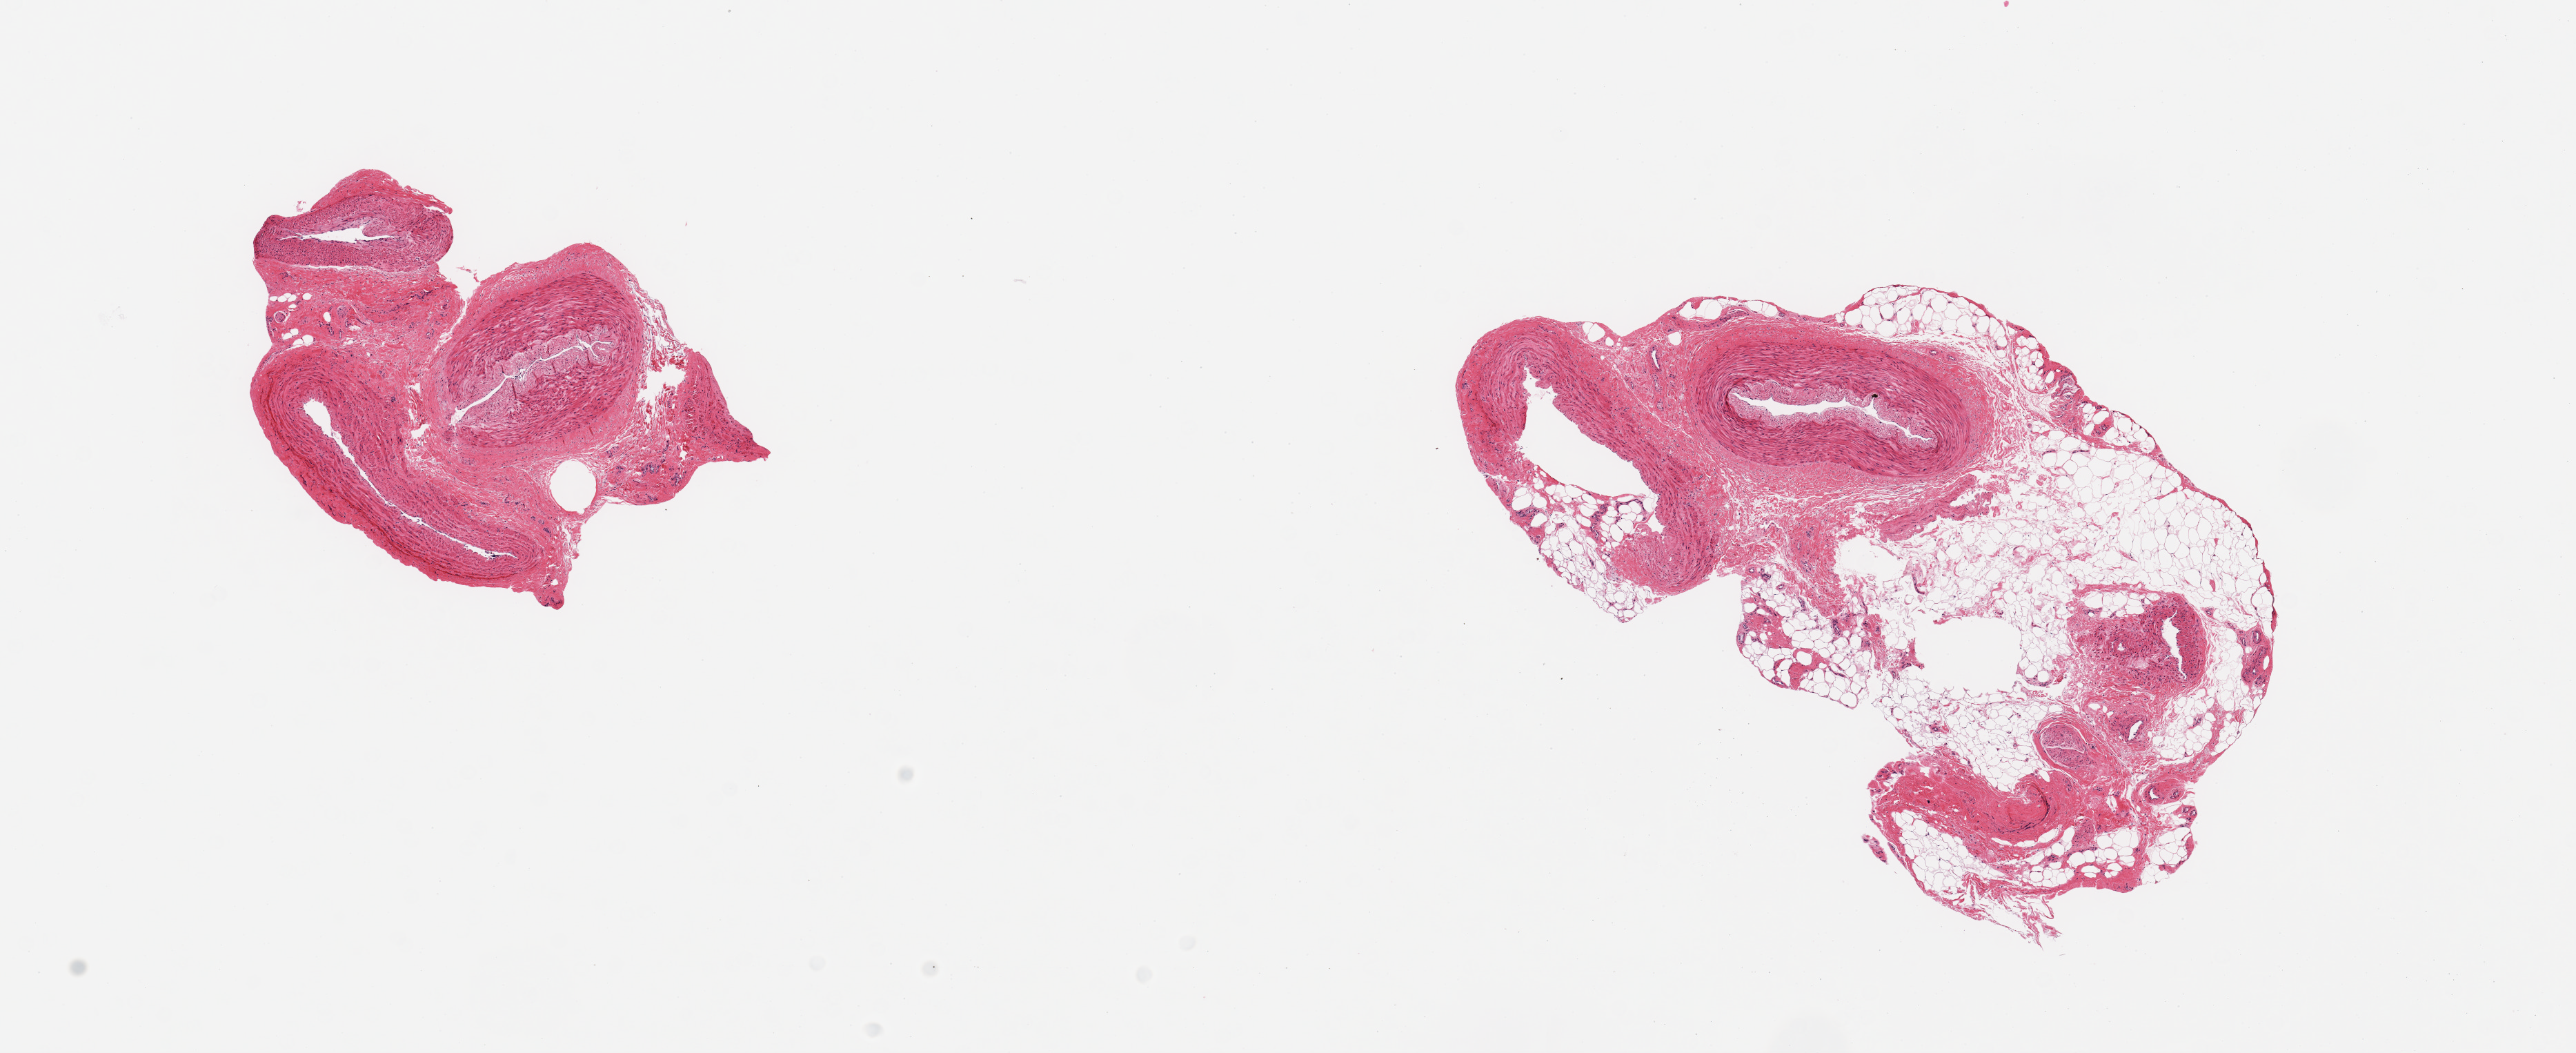
Haematoxylin and eosin whole-slide image — low-resolution overview of the scanned area, about 14.8 x 6.0 mm (acquisition: 20x scan). PAXgene-fixed paraffin-embedded (PFPE) section. Section of tibial artery (target tissue). Donor tissue sample. Donor: male.
• review note (as recorded): 2 pieces: 1 well trimmed, other with 60% fatty, neural and fibrous stroma